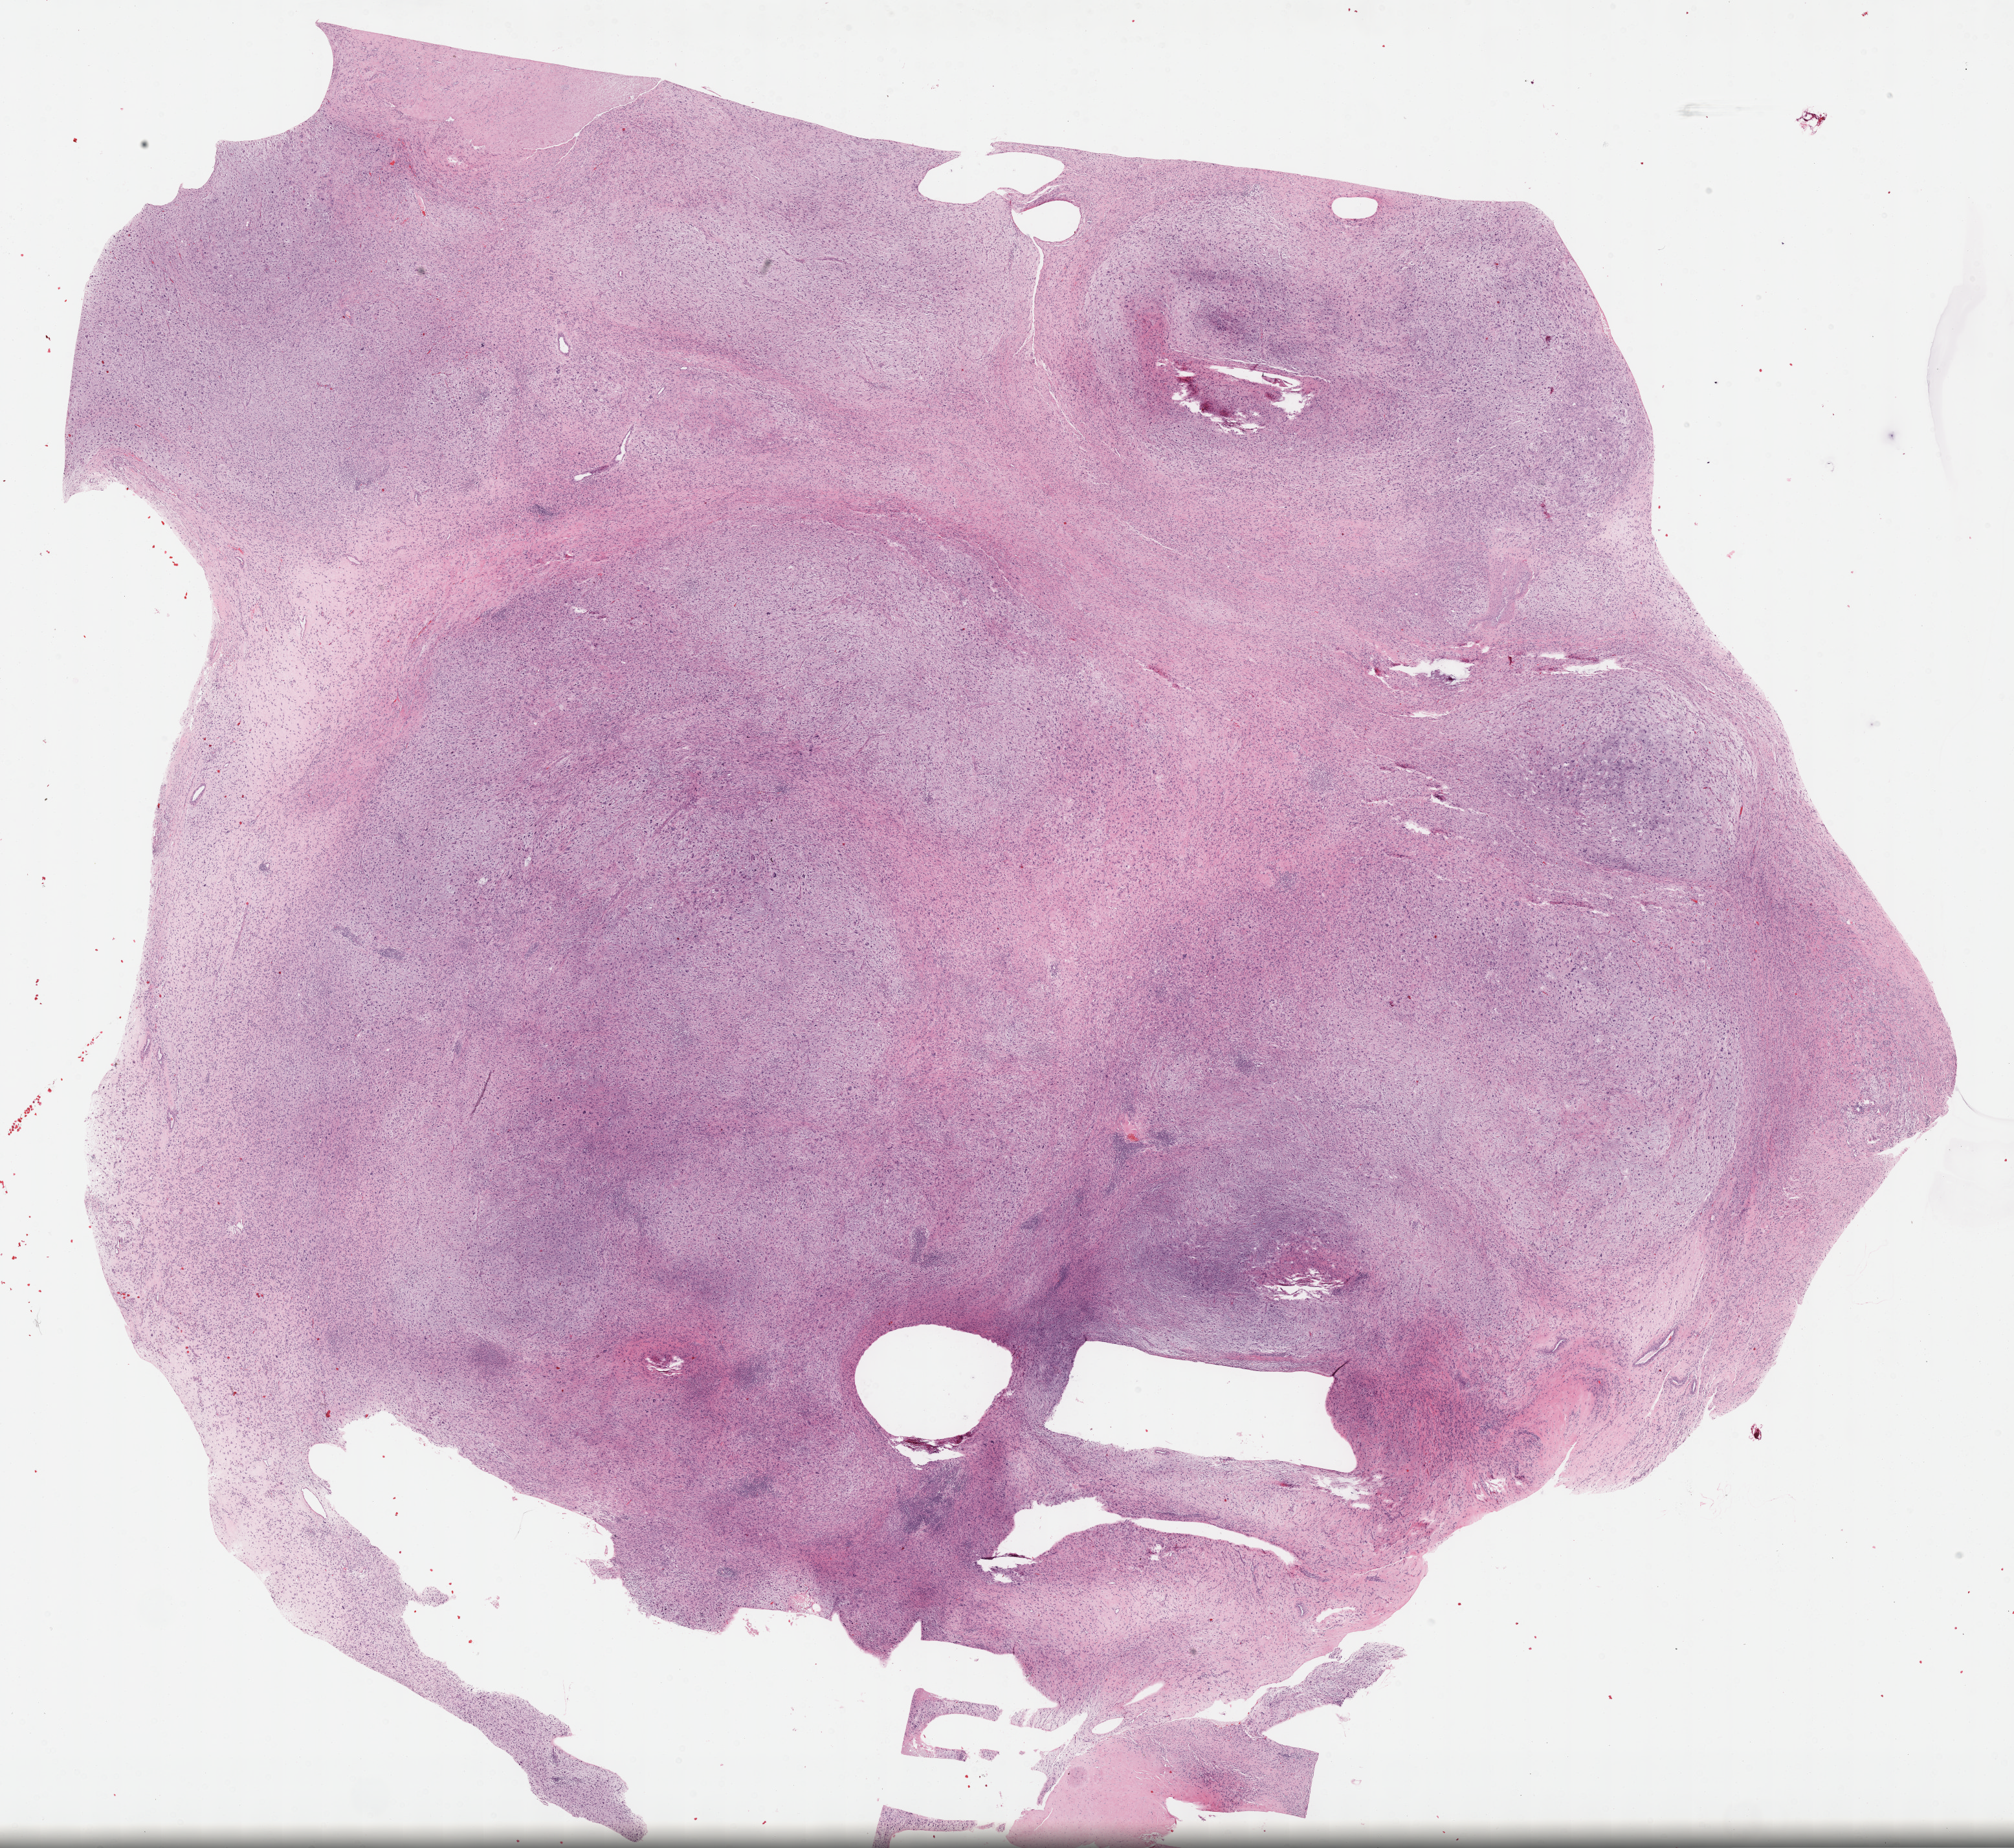
Digitized Hematoxylin and eosin (H&E) stained tissue section (whole slide) — a low-resolution overview of the entire scanned area, about 25.2 x 23.1 mm (slide scanned at 40x), formalin-fixed paraffin-embedded (FFPE) diagnostic section, sample: primary tumour, retroperitoneum and peritoneum. Patient: female, age at initial diagnosis 67 years.
• diagnosis: Dedifferentiated liposarcoma (retroperitoneum)